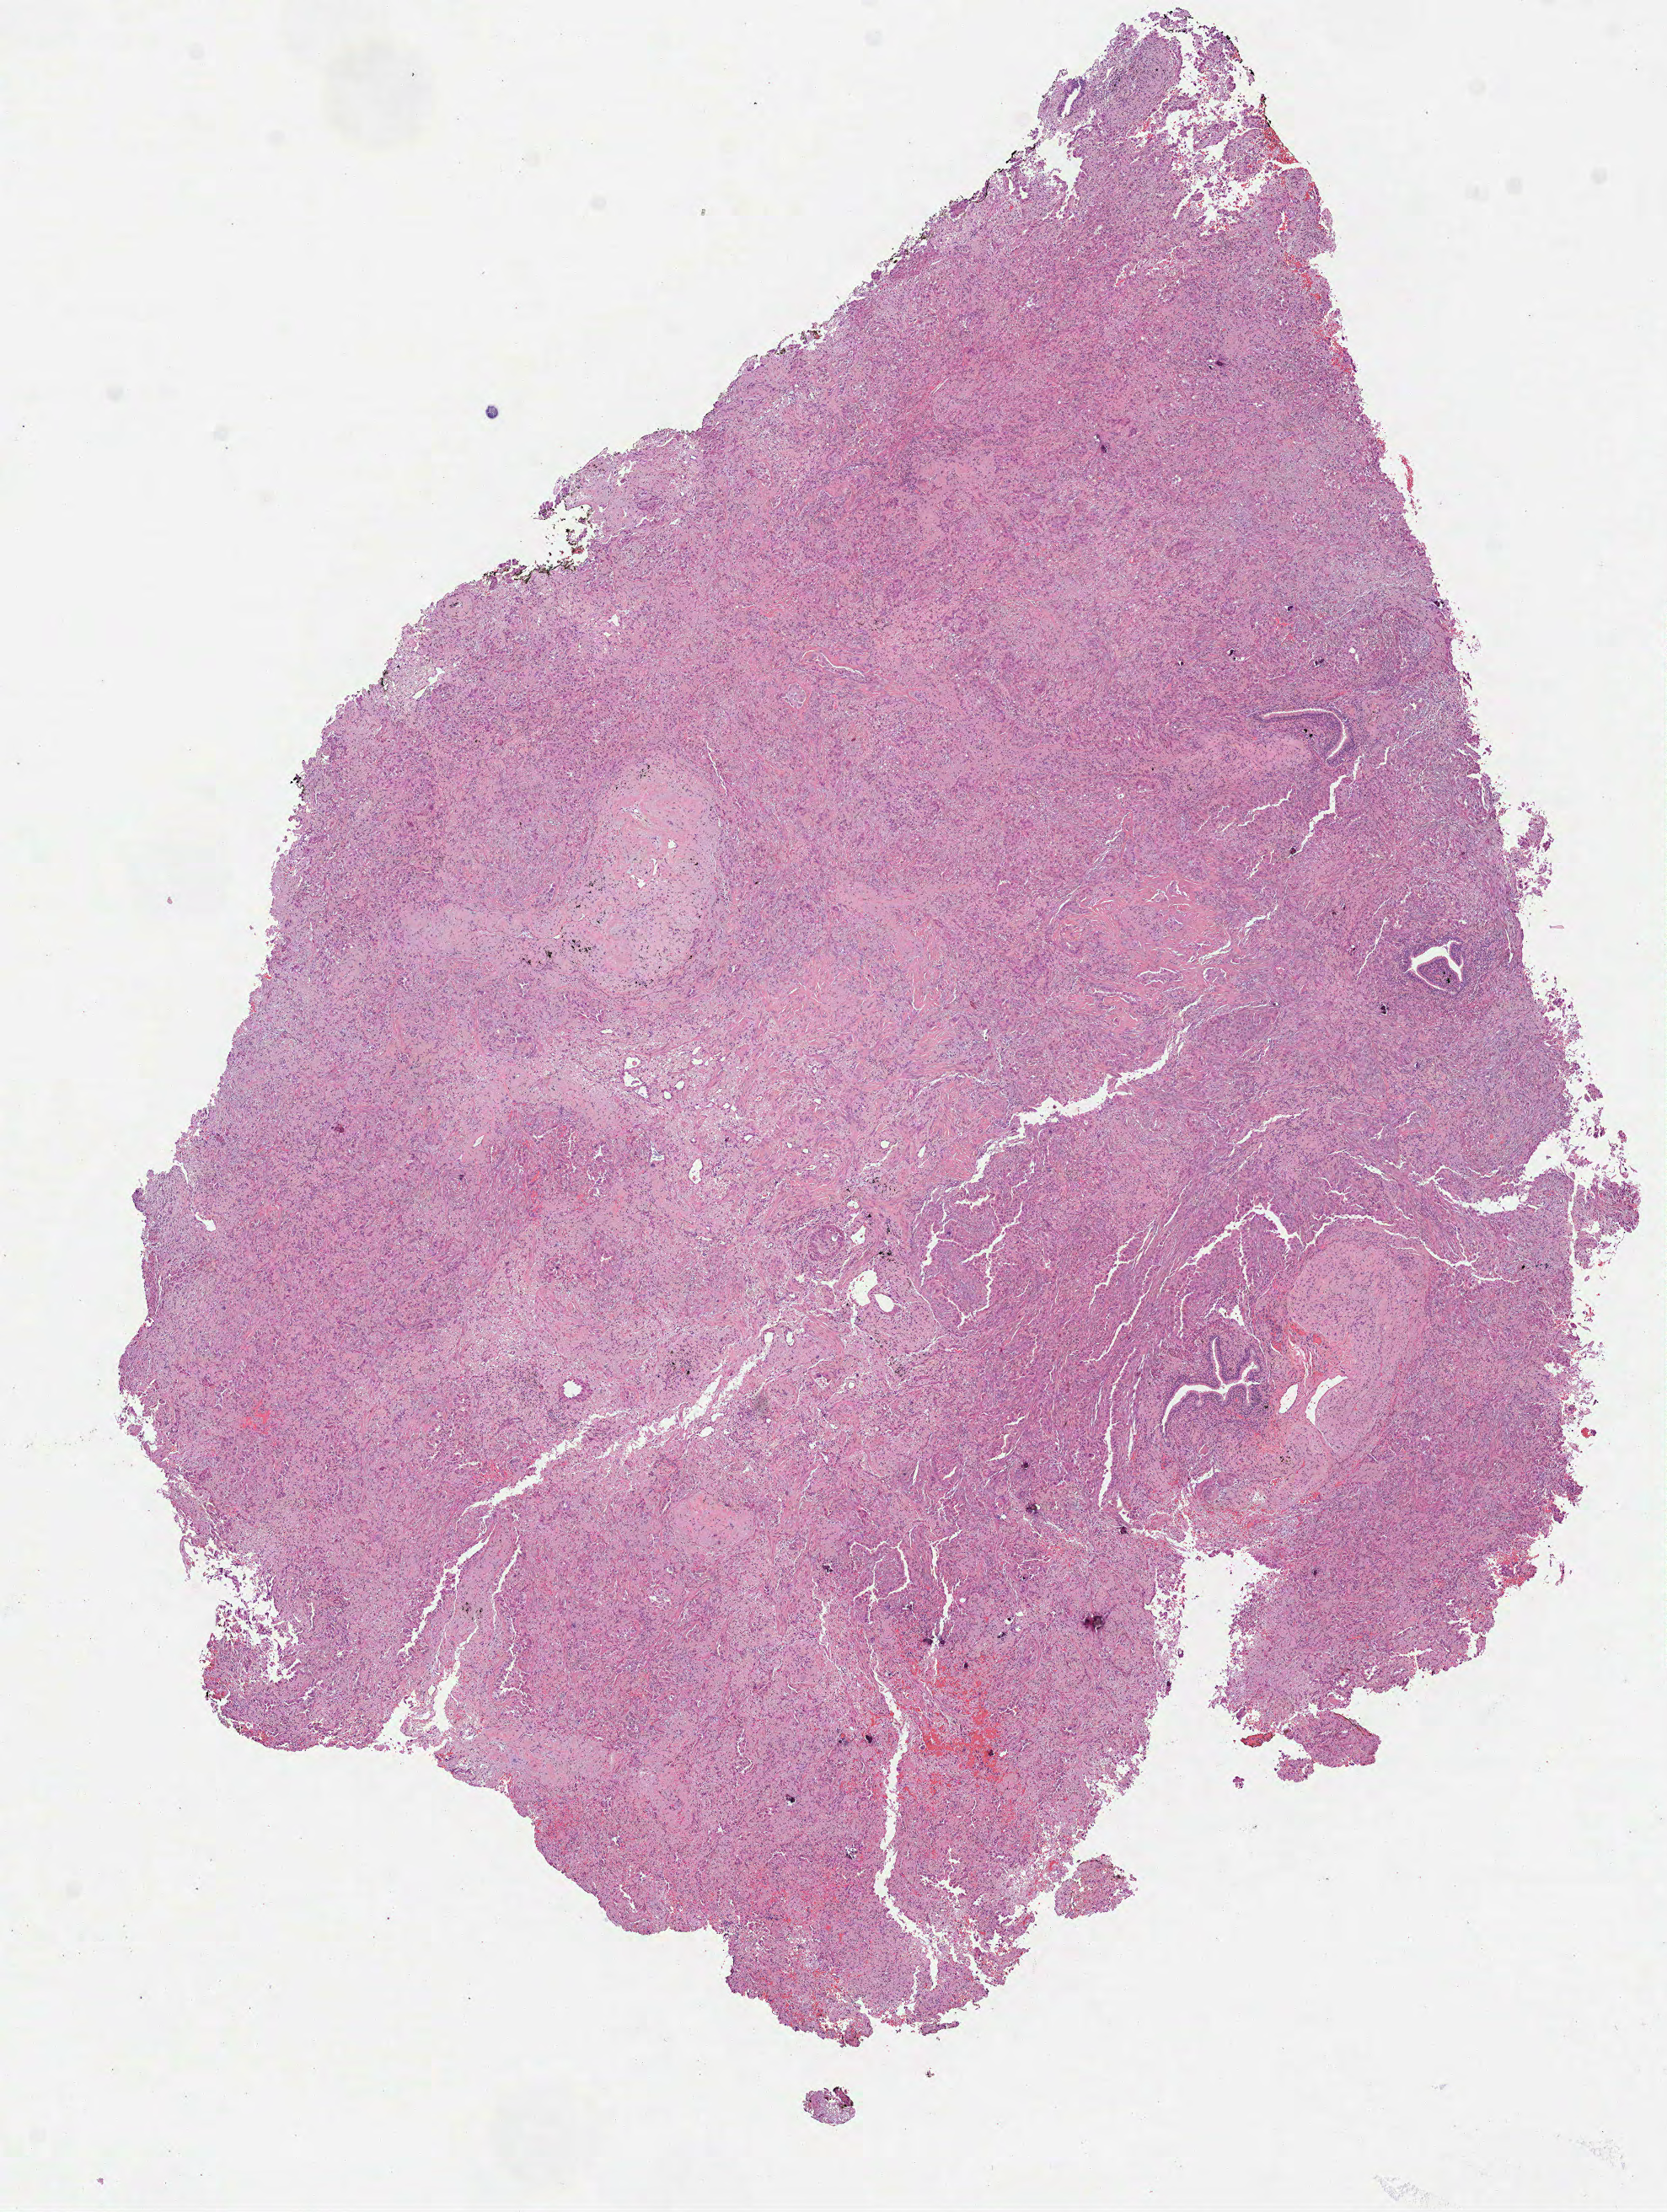
Whole-slide histology image, Hematoxylin and eosin (H&E) stained, low-resolution overview of the scanned area, about 8.0 x 10.6 mm (from a 40x scan), formalin-fixed paraffin-embedded (FFPE) diagnostic section, lung, primary tumour sample. Patient: female, age at initial diagnosis 53 years.
TNM: T1 N2 M0. AJCC pathologic stage: IIIA (6th edition). Laterality: left. Pathologic diagnosis: Adenocarcinoma, NOS (upper lobe, lung).